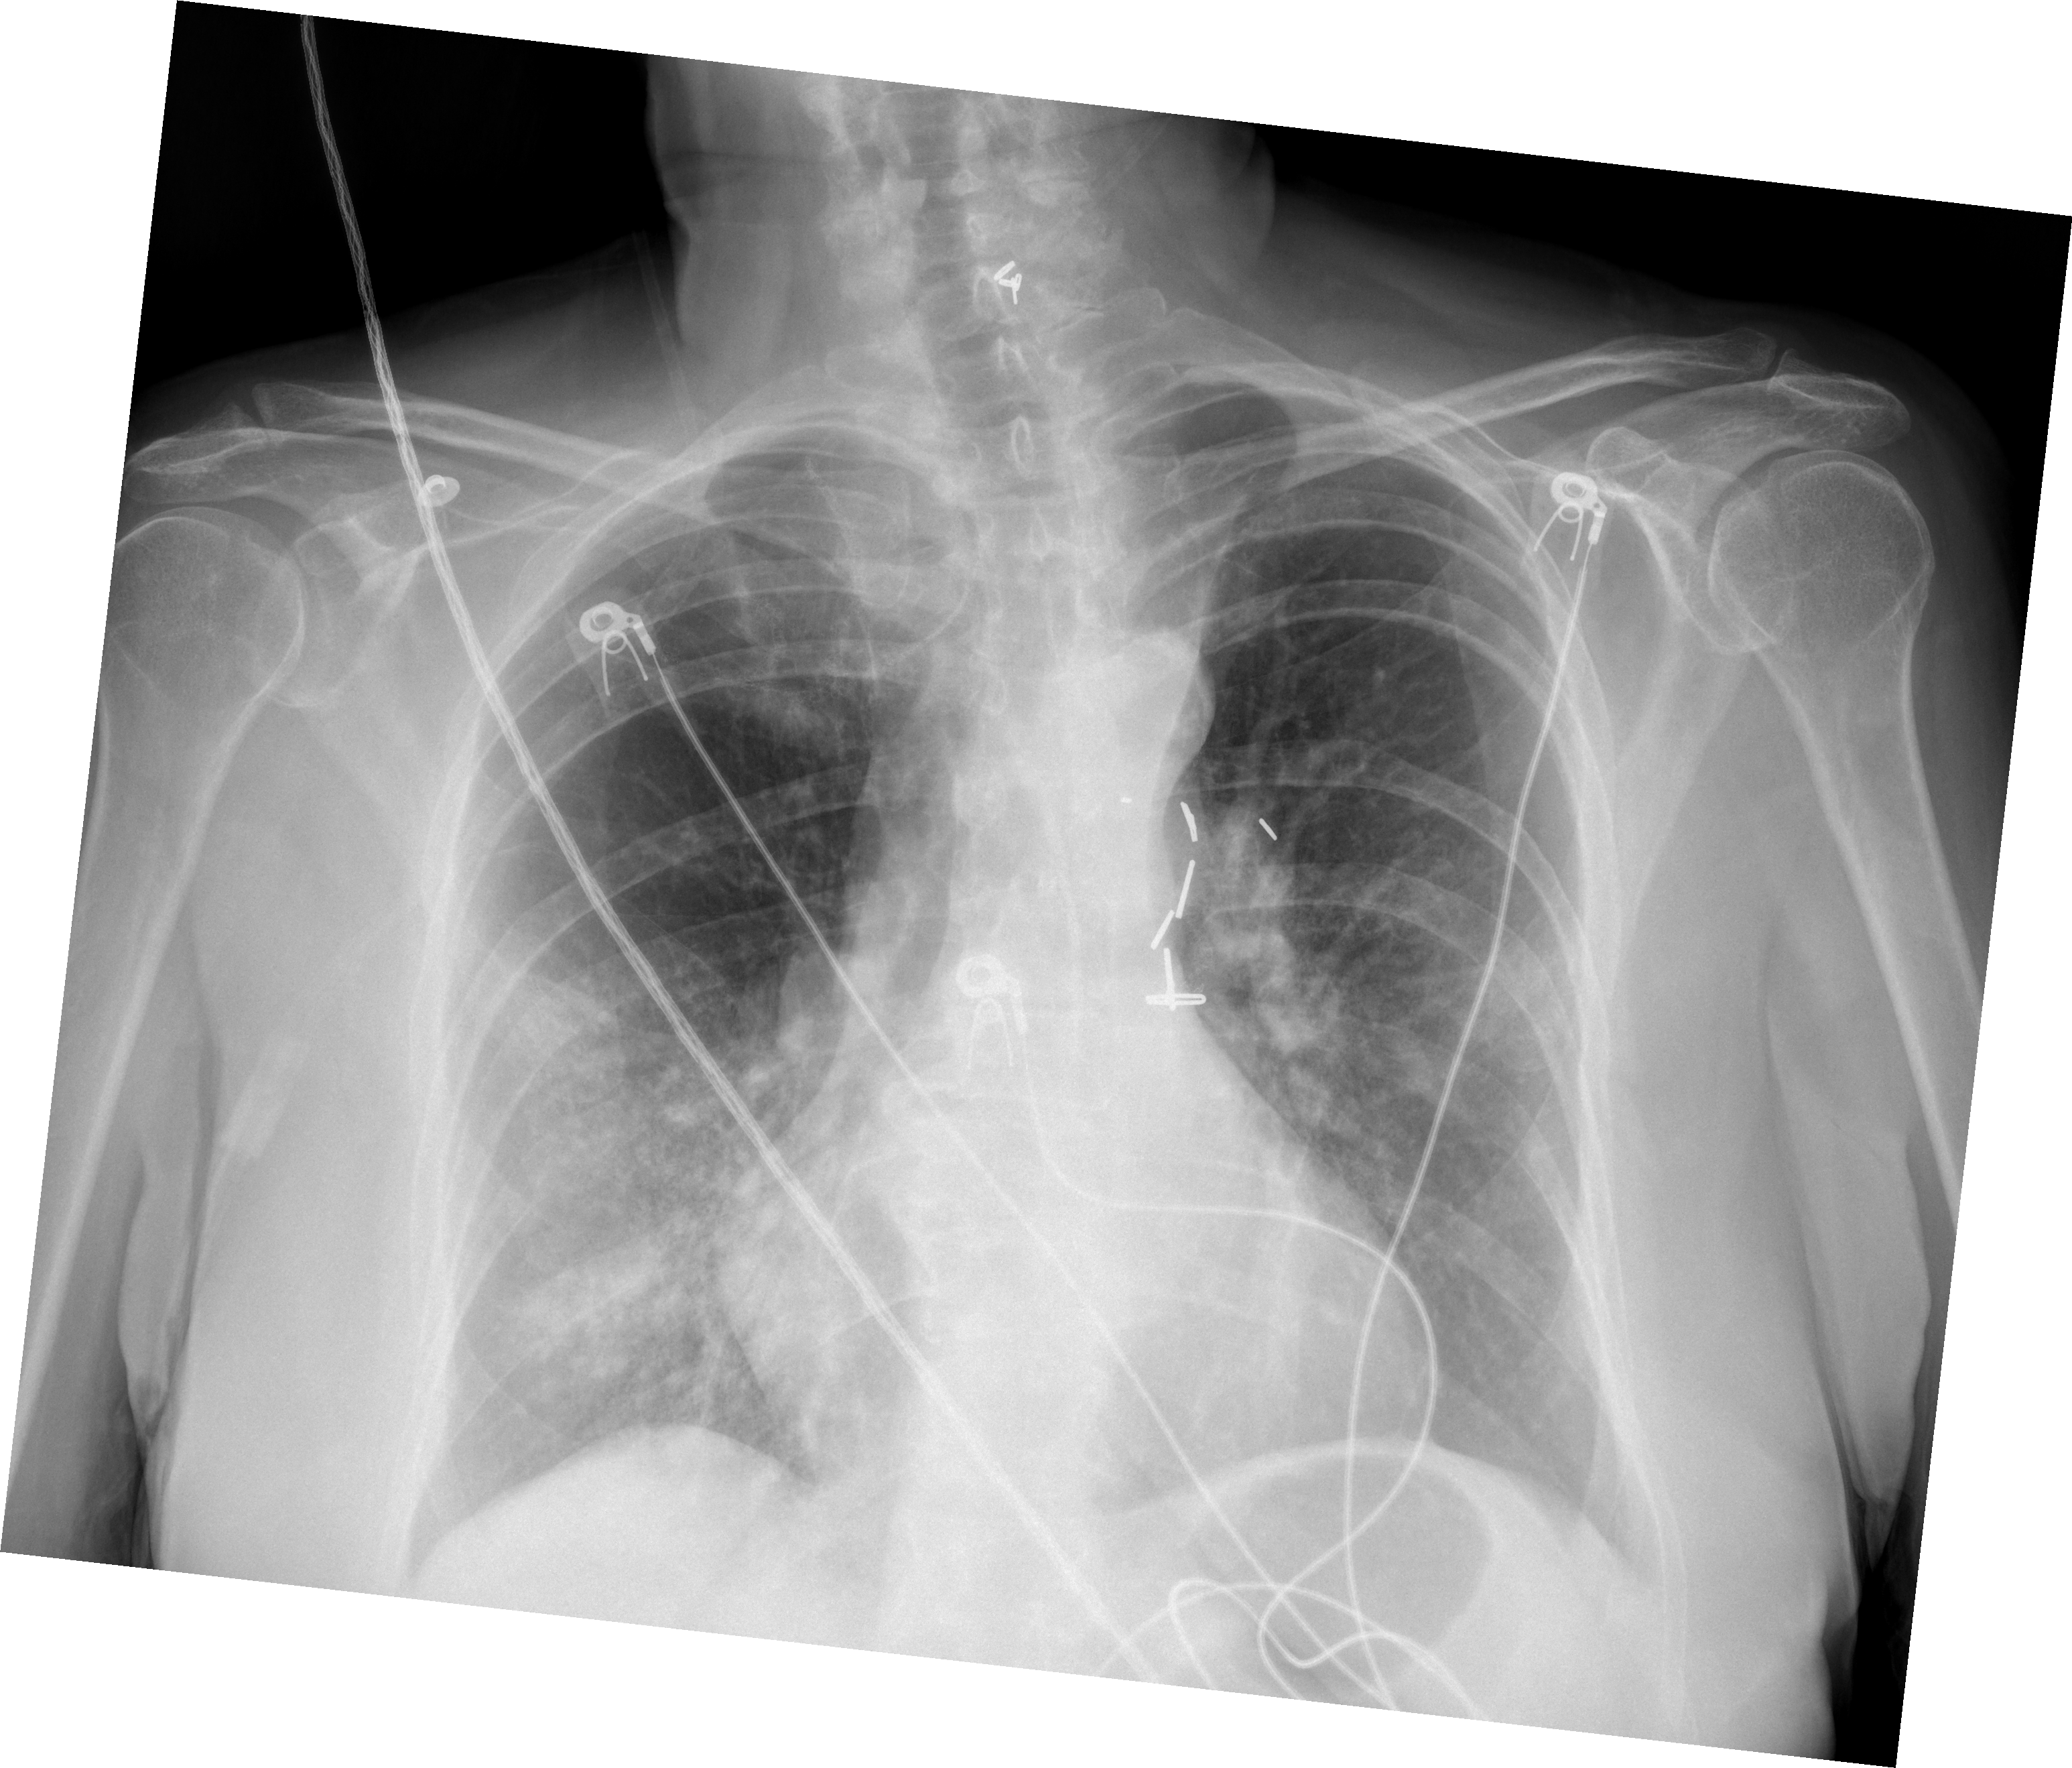
Chest X-ray (portable), AP projection. Female patient, age 72 years; imaged 1 day after the COVID-19 diagnosis.
Key findings recorded by the radiologist: Hazy airspace opacities are seen throughout the bilateral lower lungs, right greater than left.